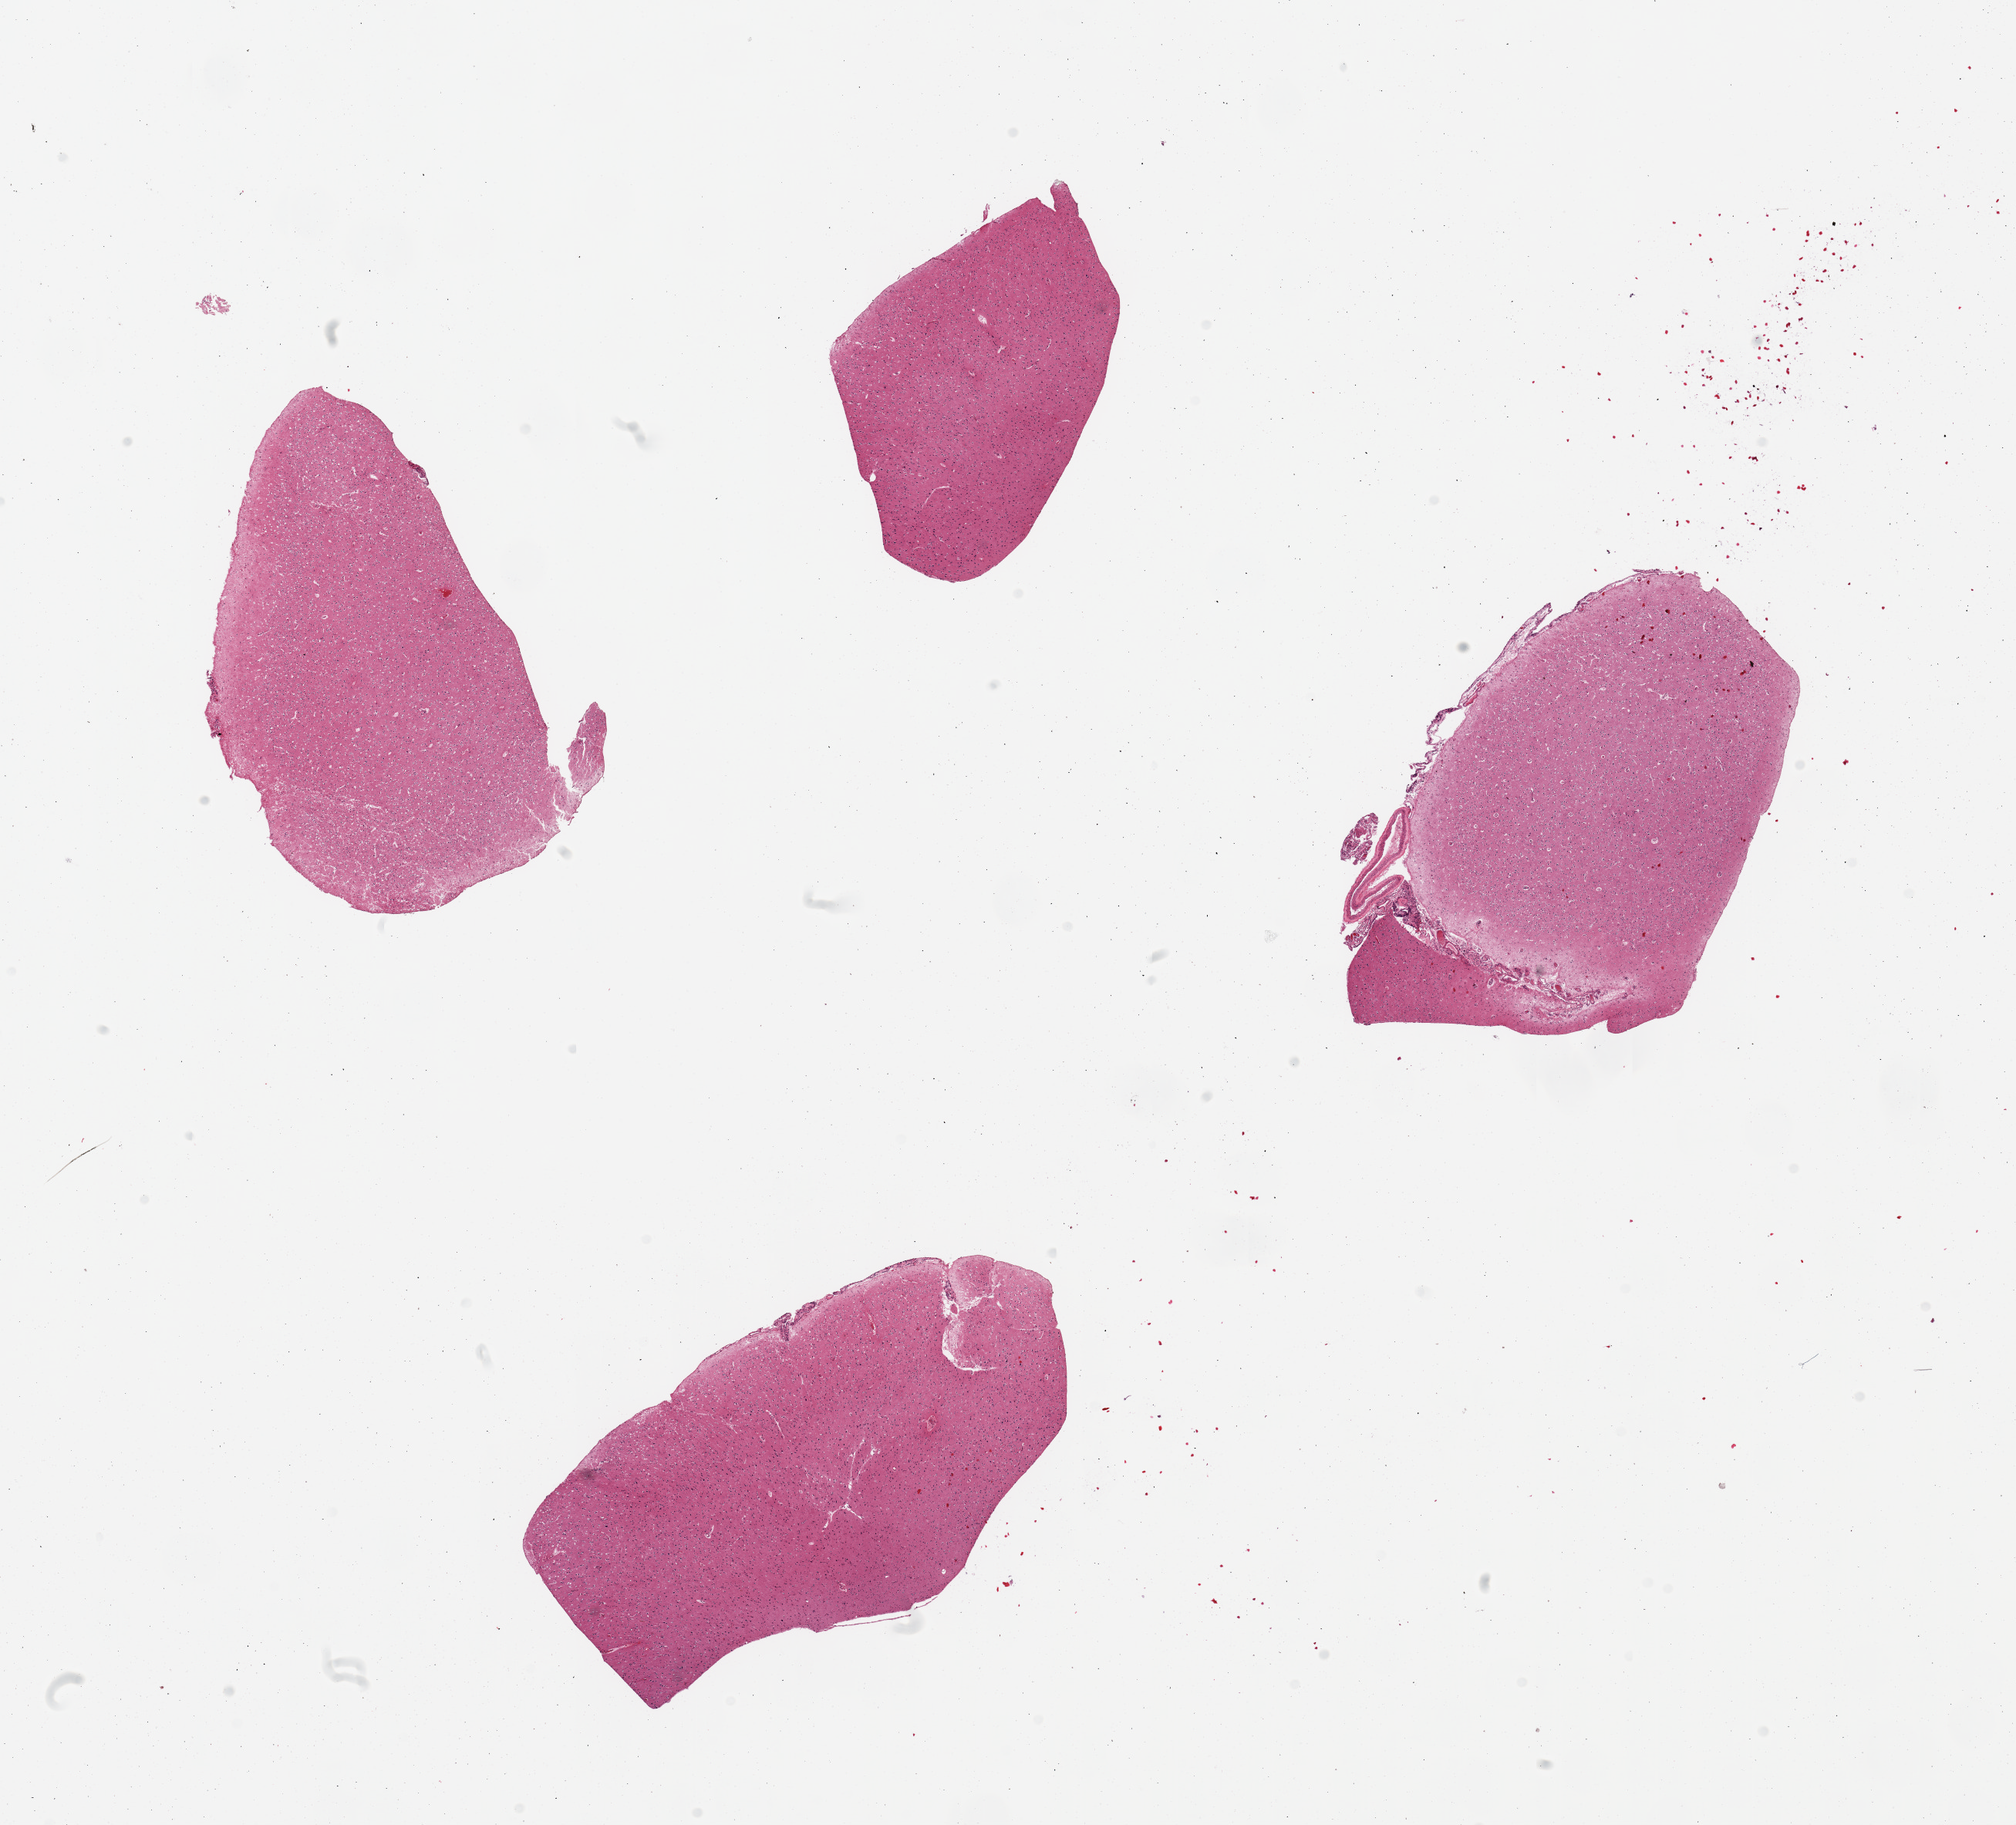
Hematoxylin and eosin (H&E) whole-slide image, whole scanned area (about 20.7 x 18.7 mm, from a 20x scan) shown as a low-resolution overview, PAXgene-fixed, paraffin-embedded tissue, sampled site (target tissue): cerebral cortex, tissue donor sample. Donor sex: female.
Pathologist's review note for this sample: 4 pieces; meningeal vessels on 1 piece.